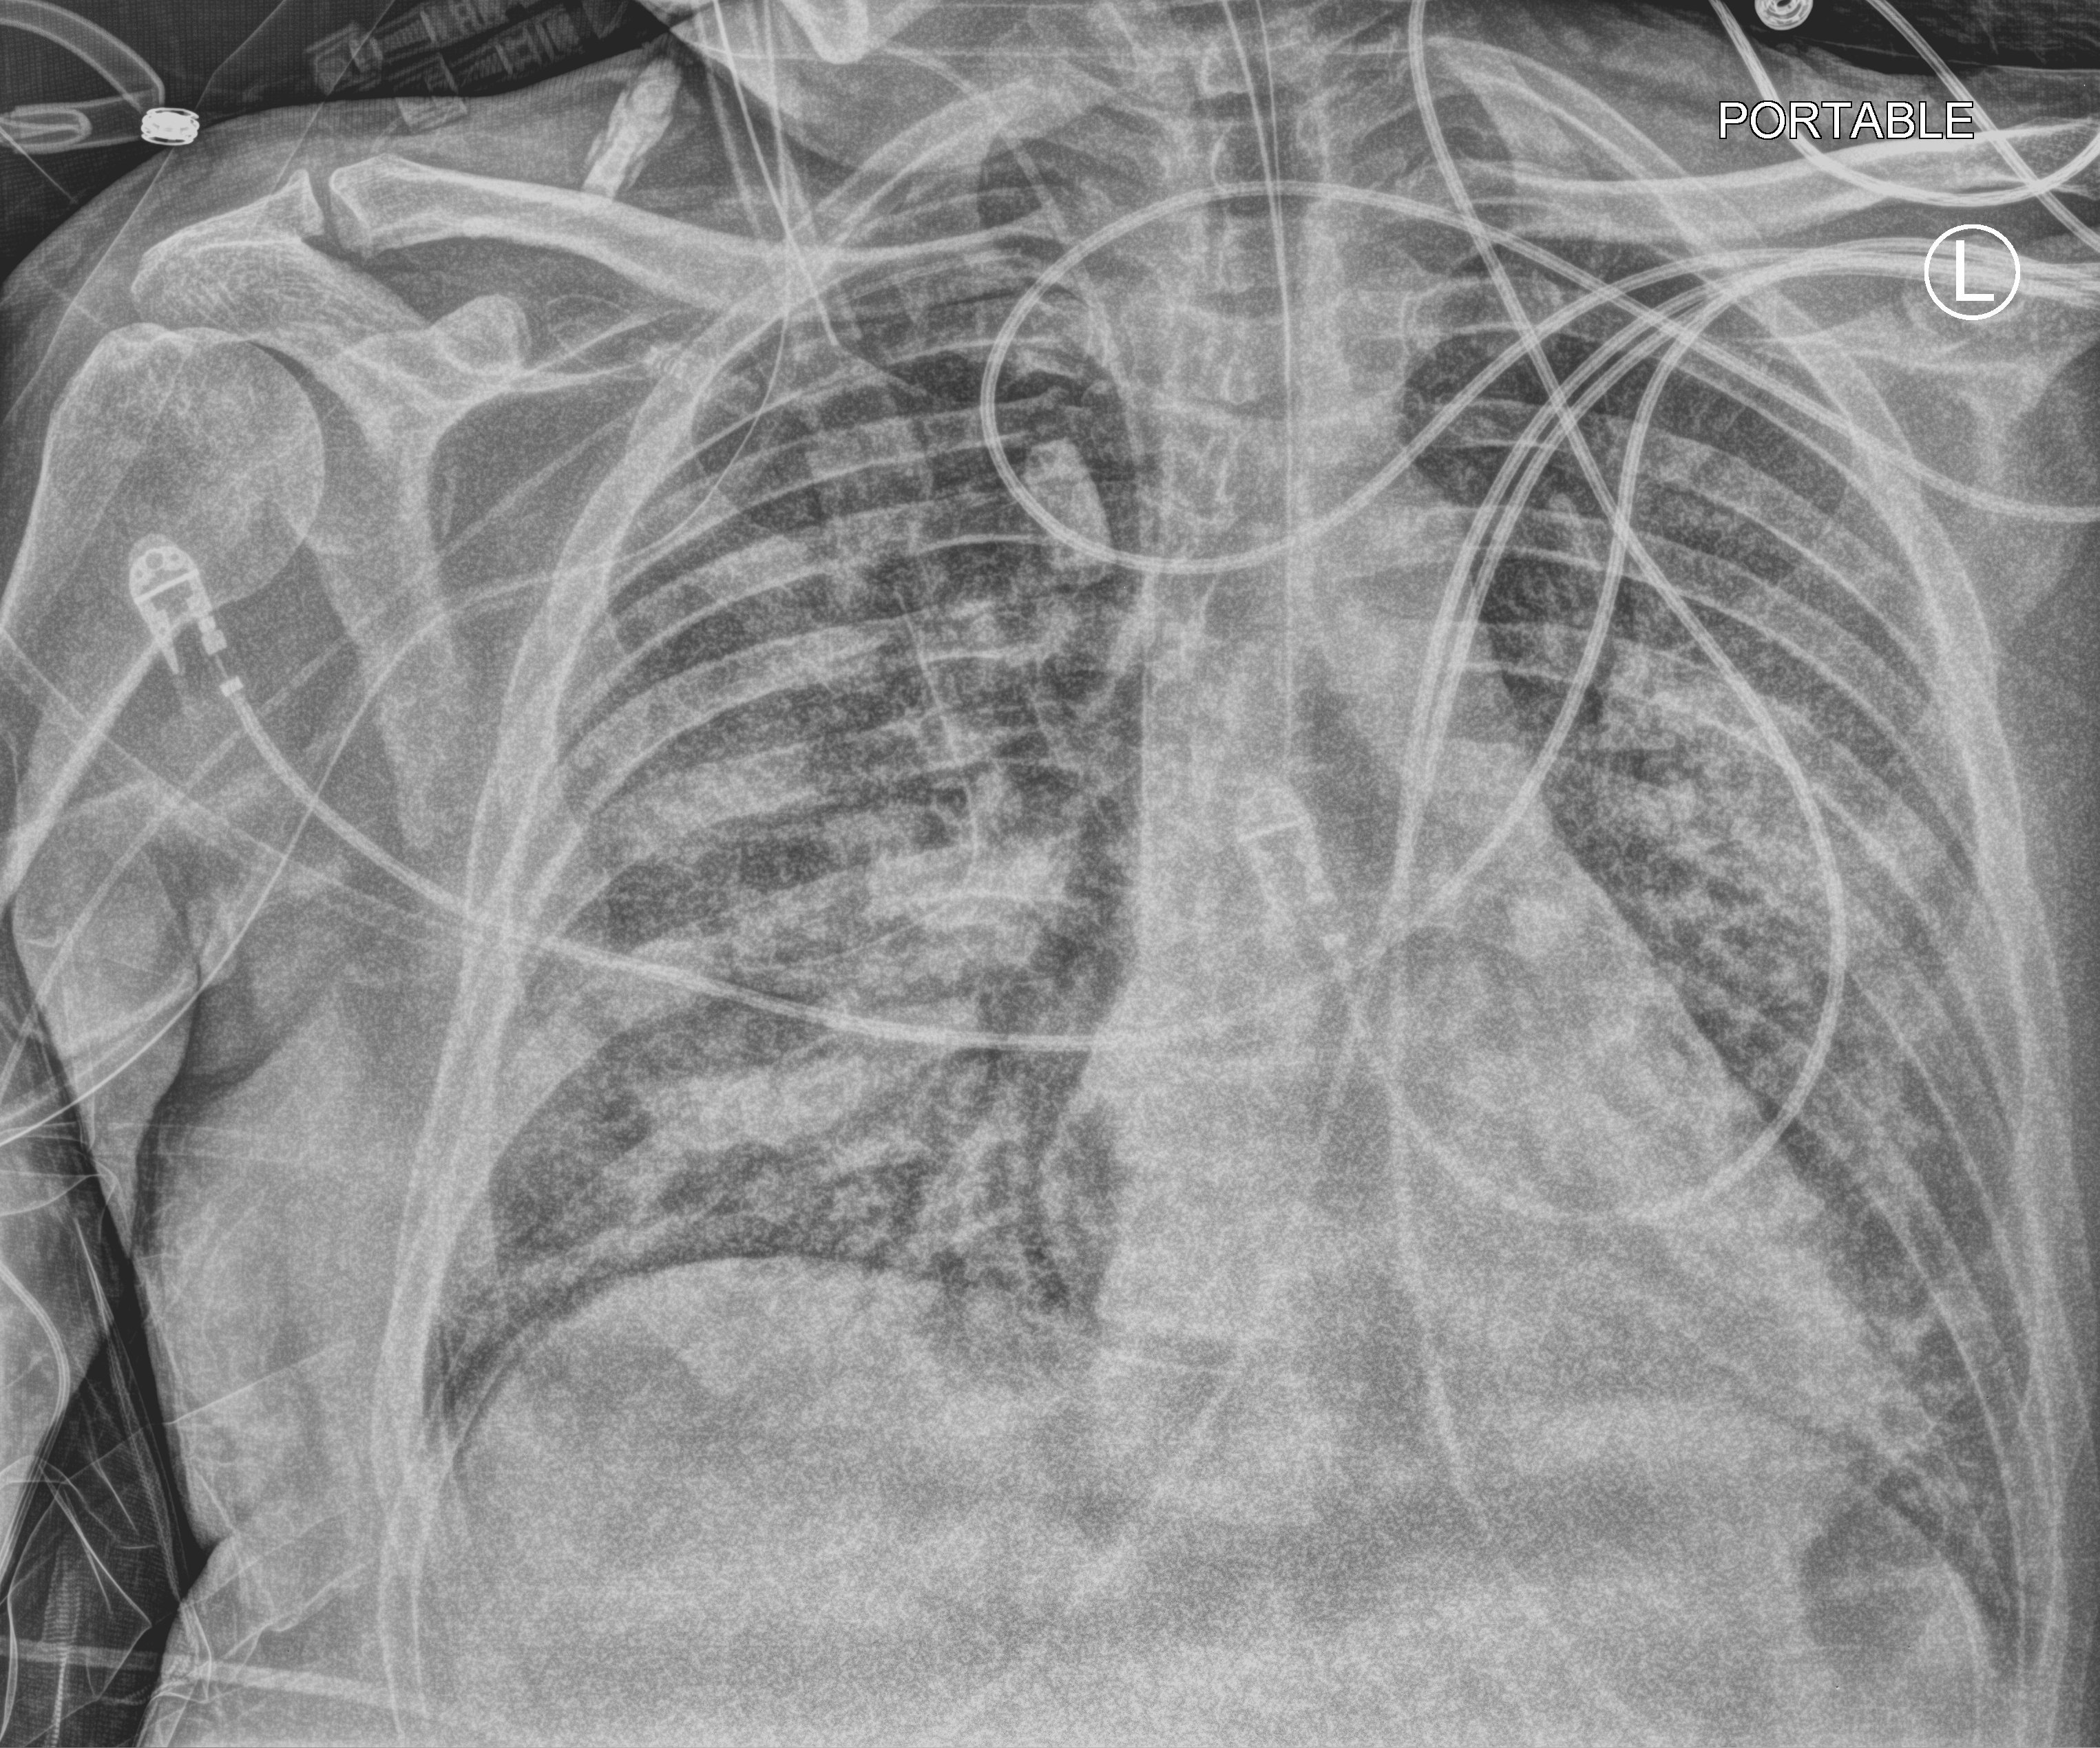
Bedside chest radiograph (computed radiography); anteroposterior (AP) projection. Patient hospitalised with COVID-19; male, aged 18–59 years.
Admission-level facts for this patient (not findings on this image; timing relative to this image not recorded):
- other chronic lung disease (admission record): no